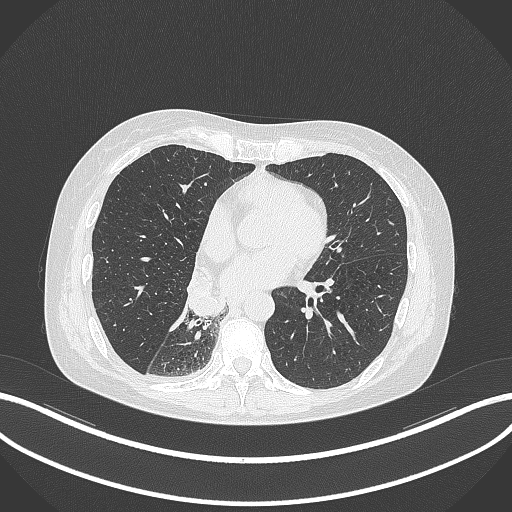
Chest CT, one axial slice. Position 129 of 329 along the scan axis. 120 kVp. Lung window (W 1500 / L -600 HU). 1 mm slice thickness. 512 × 512 image matrix, field of view 400 × 400 mm. Female patient, age 63 years. From the clinical record (not read from this slice): clinical TNM (as recorded): T1c N0 M0.
Outlined on this slice (rectangle marked by the reading radiologist):
- lung tumour (recorded histology: adenocarcinoma): bounding box (x1, y1, x2, y2) in pixels: (181, 268, 226, 322)